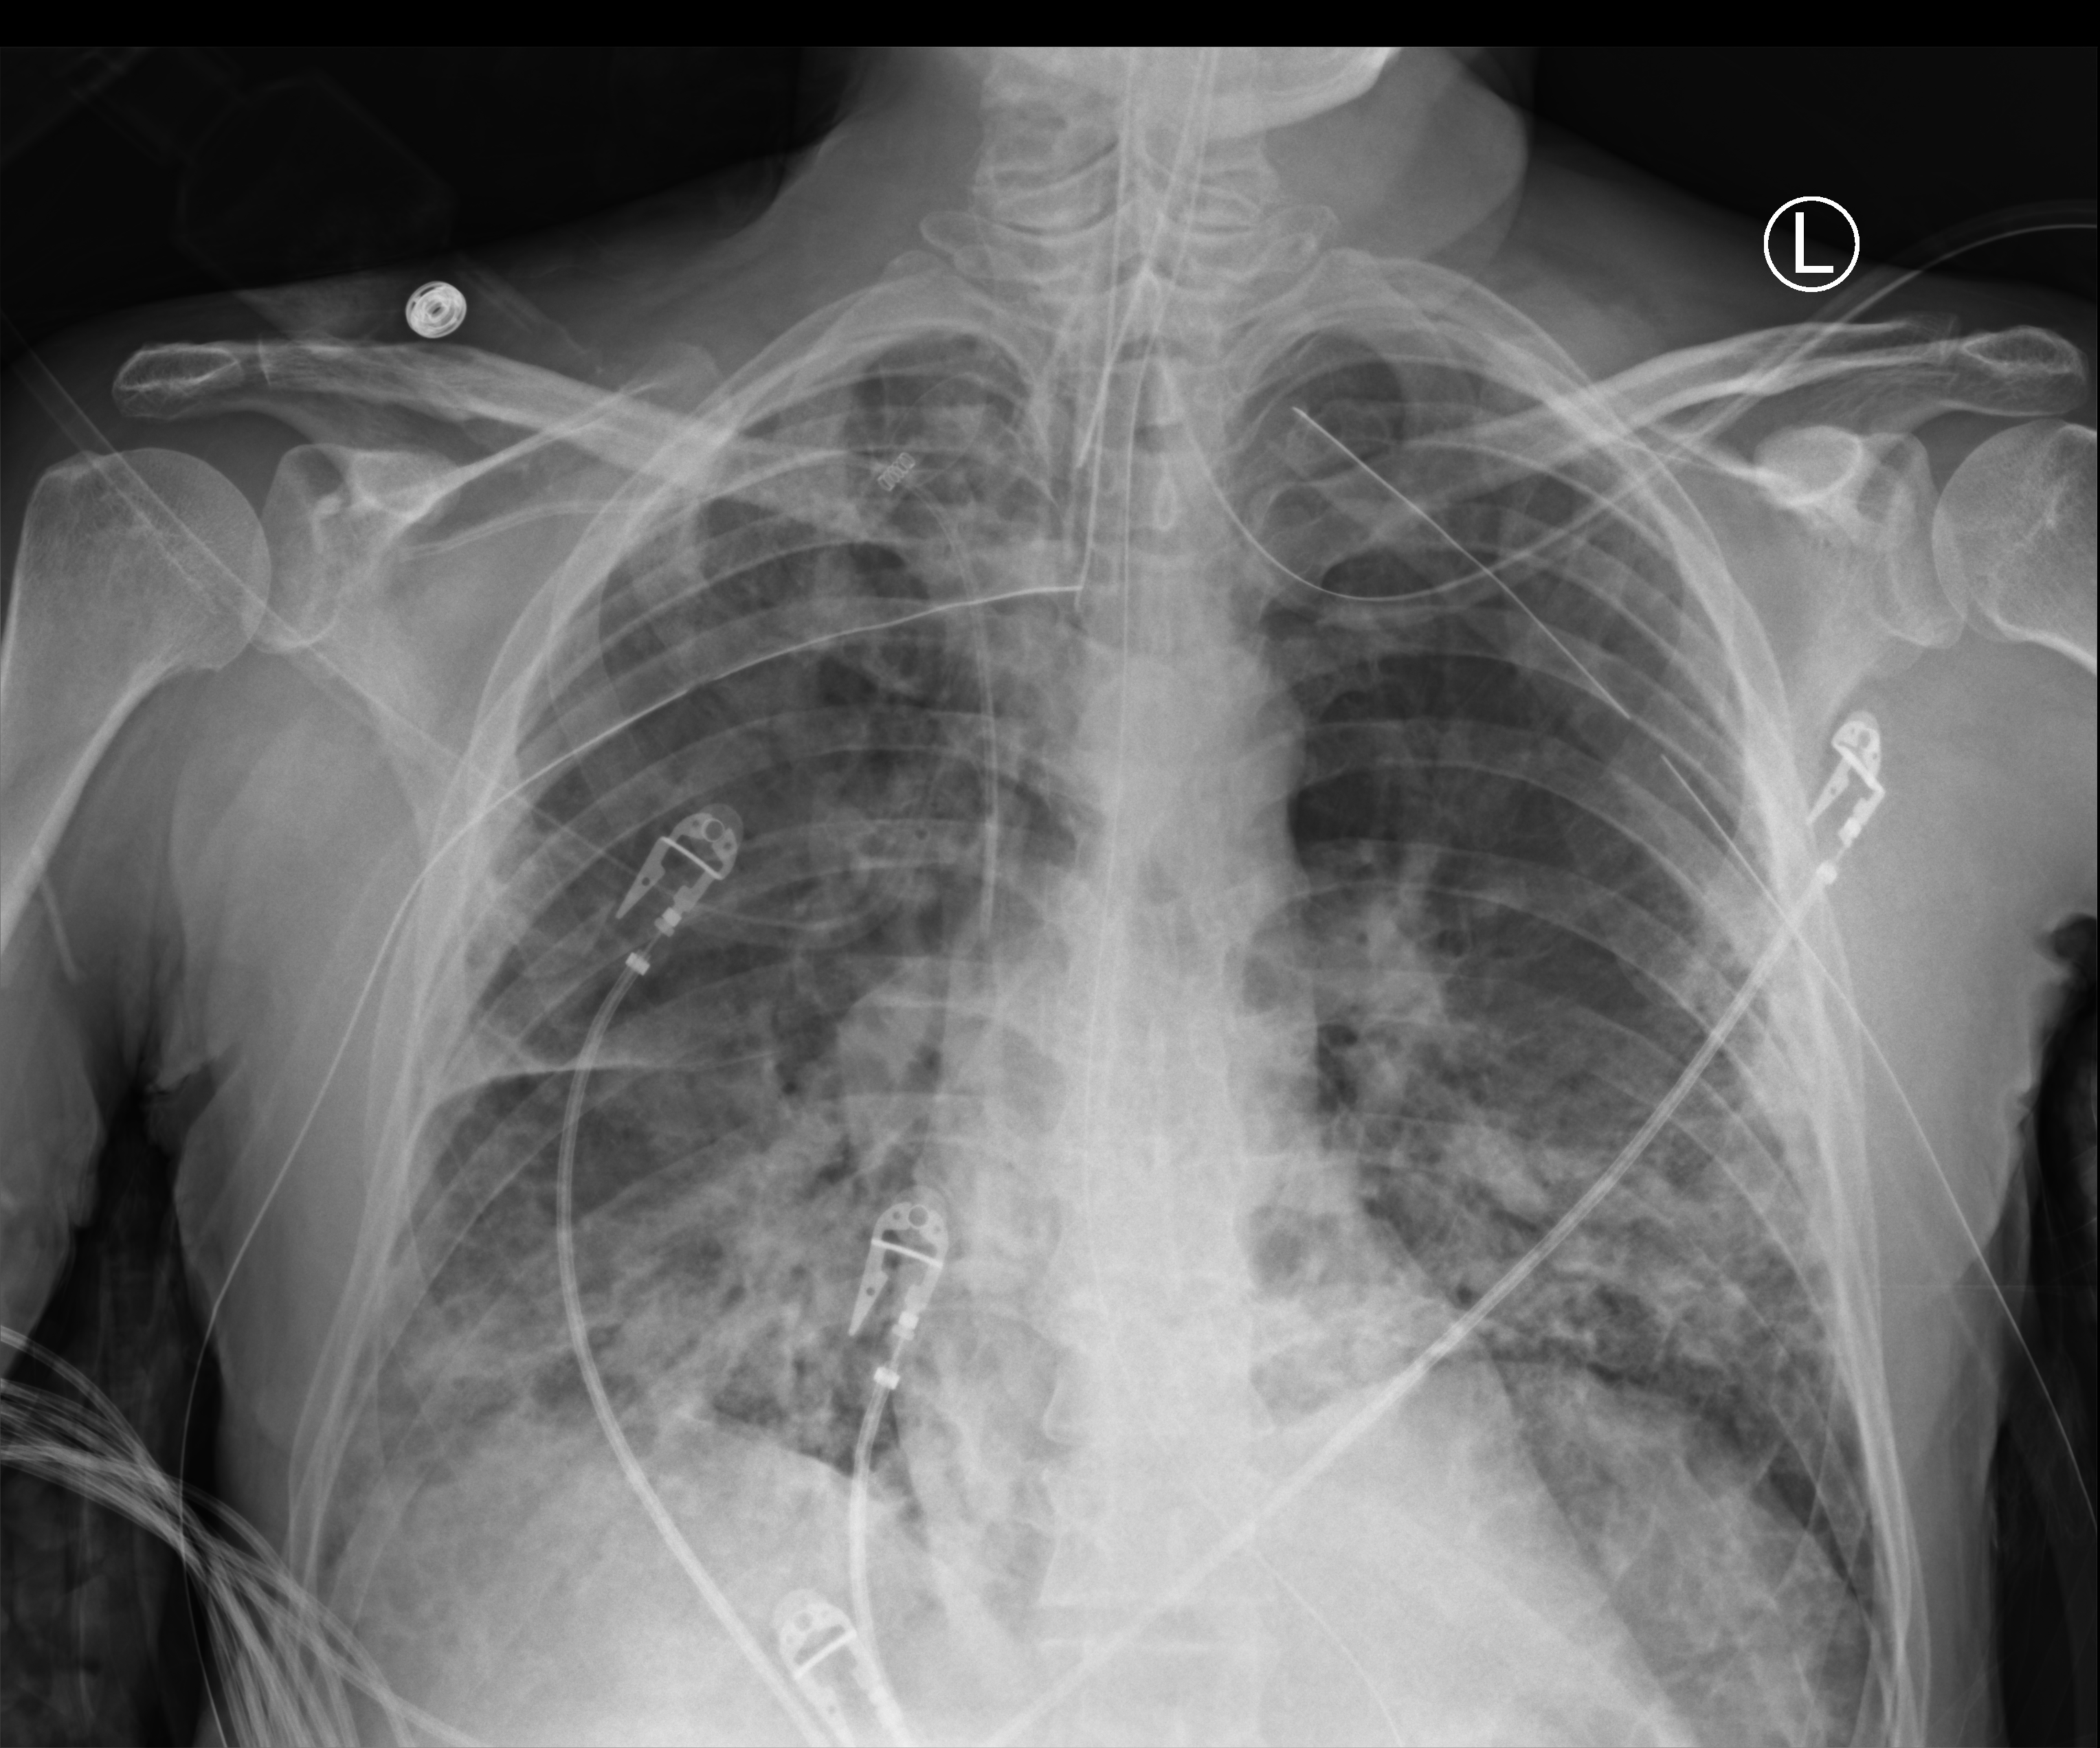
Bedside chest radiograph (computed radiography); anteroposterior (AP) projection. Patient hospitalised with COVID-19; male, aged 18–59 years.
Hospital-stay facts (about this admission, not read from this image; timing relative to this image not recorded): mechanically ventilated during this hospital stay: yes.